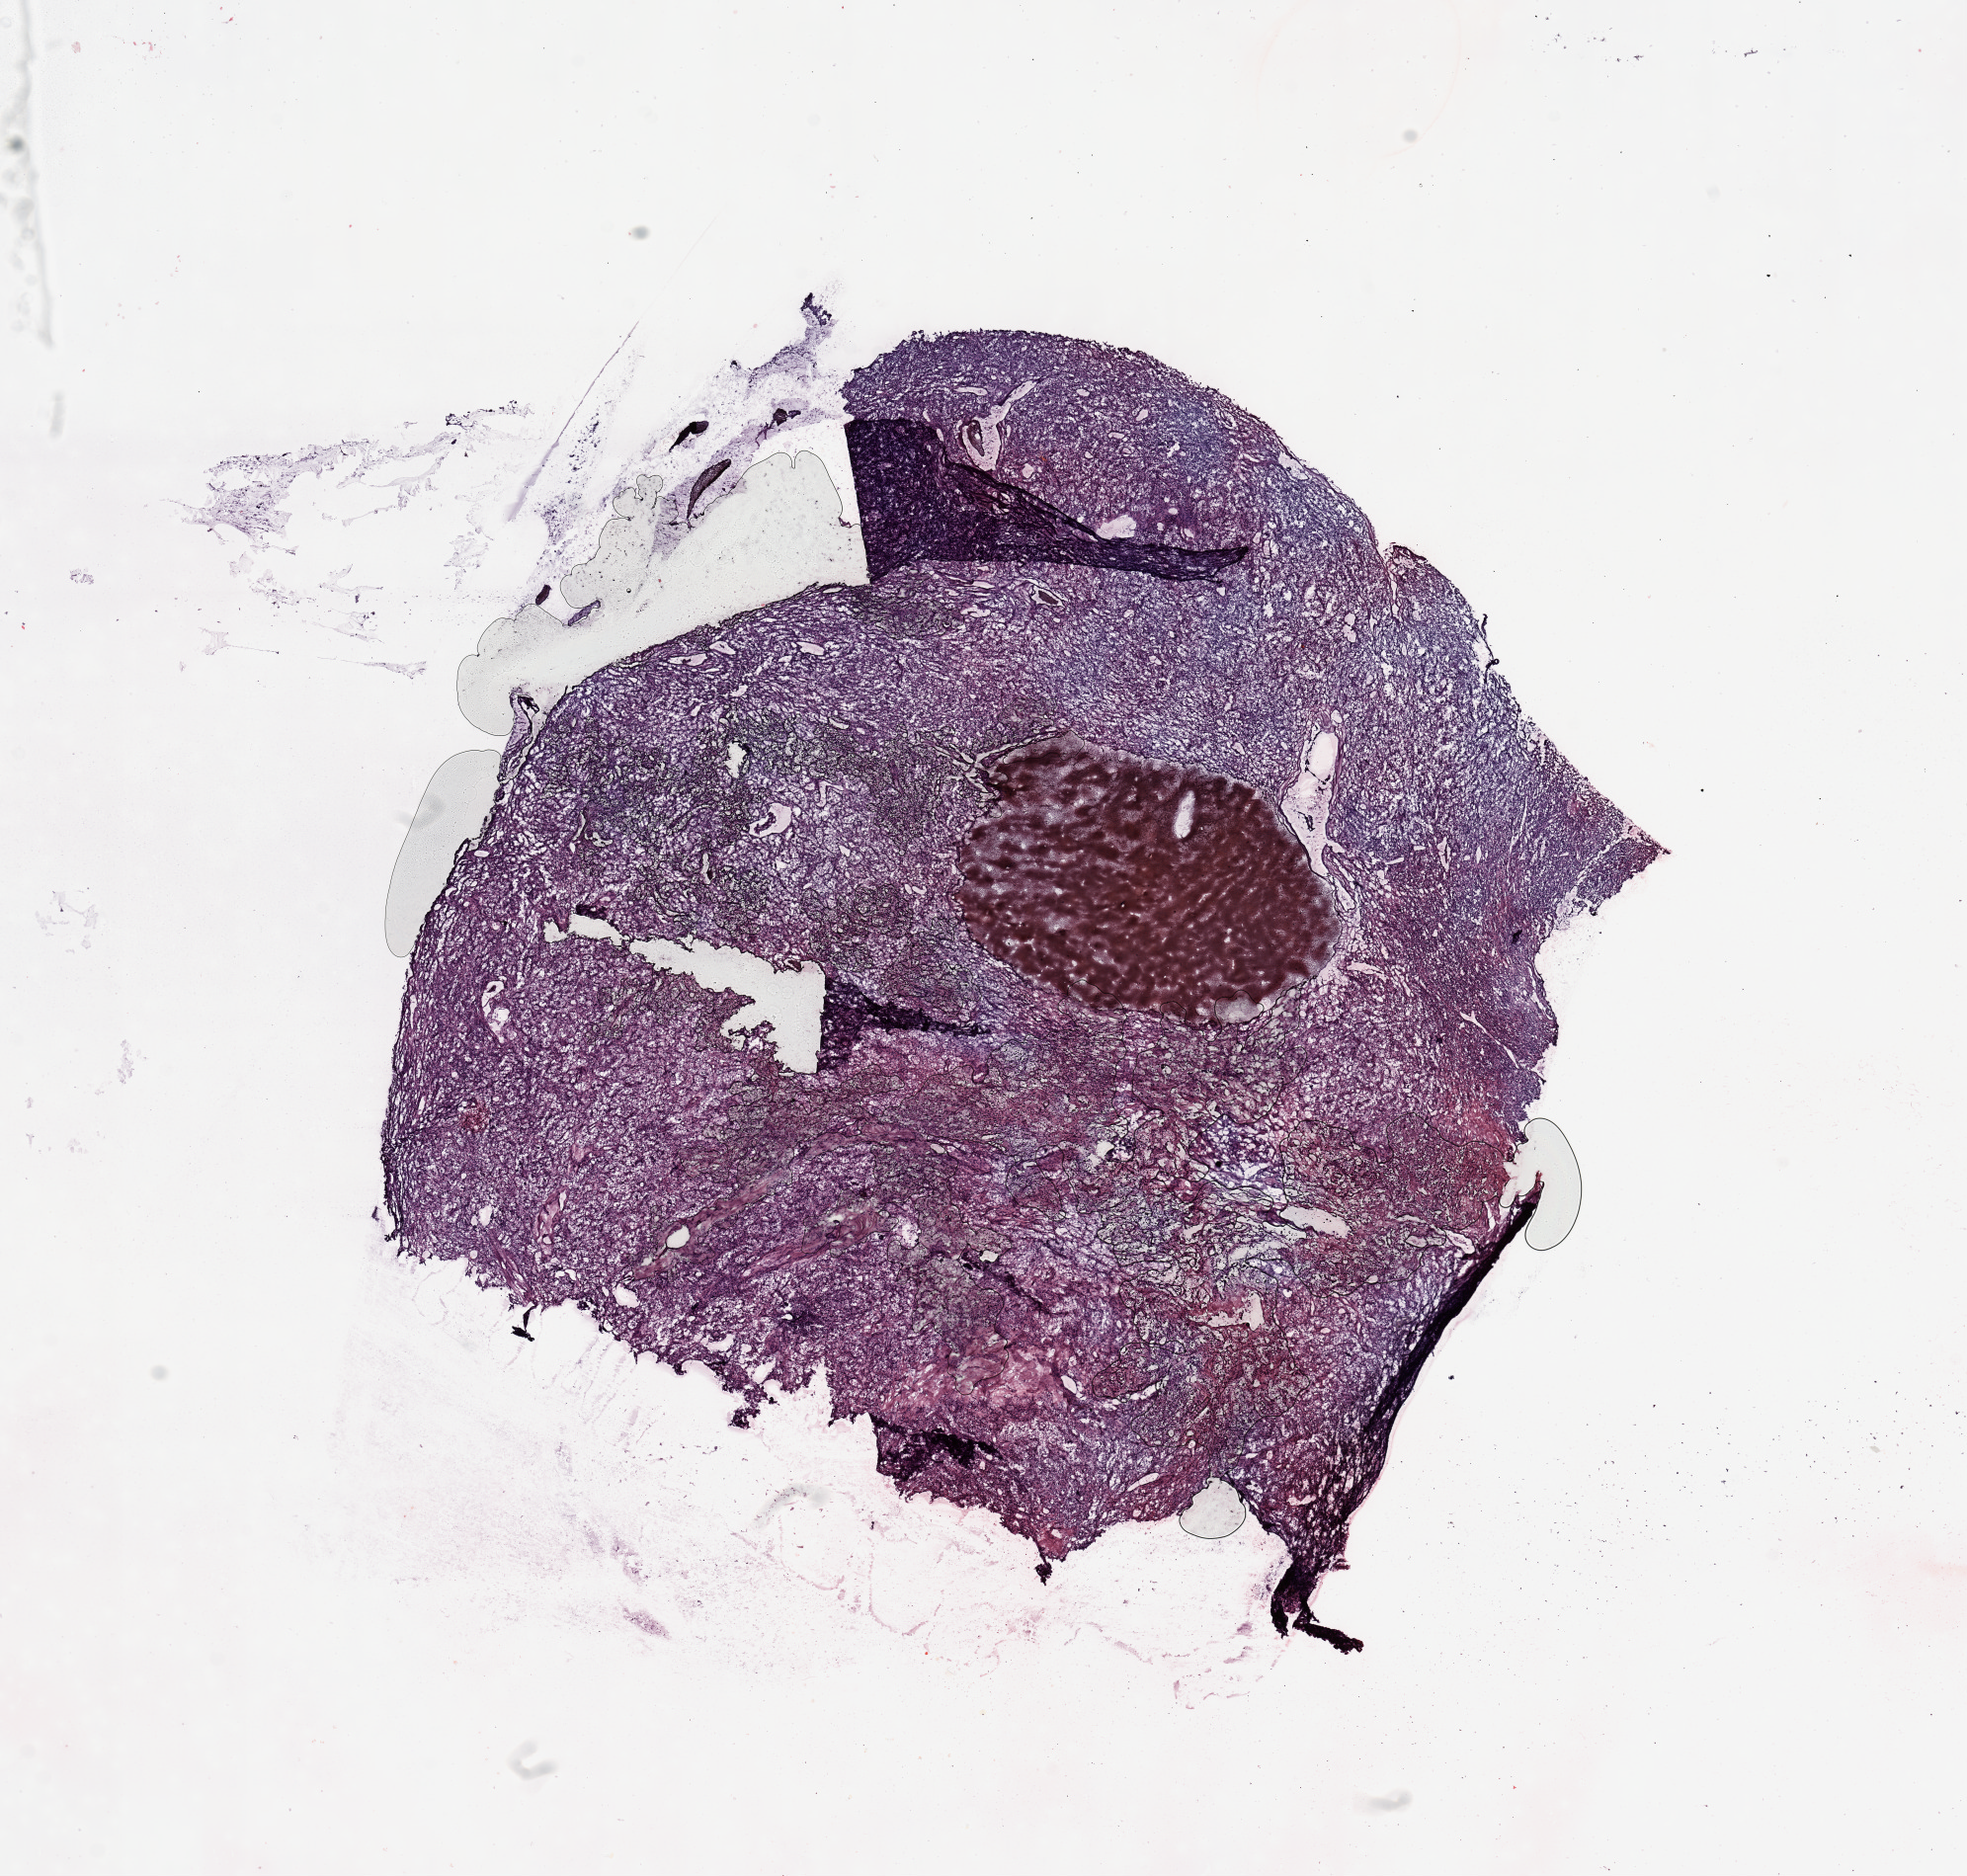
Digitized H&E tissue section (whole slide), low-resolution overview of the scanned area, about 15.8 x 15.0 mm (from a 20x scan), tumour tissue sample, sampled site: kidney. Patient: male, age 58 years. Histologic grade: G2 (moderately differentiated). Composition of this section per pathologist review: tumour nuclei 90%, necrosis 5%.
AJCC pathologic stage: IV. Primary tumour site (as recorded): upper pole. Histologic diagnosis: Renal cell carcinoma, NOS.